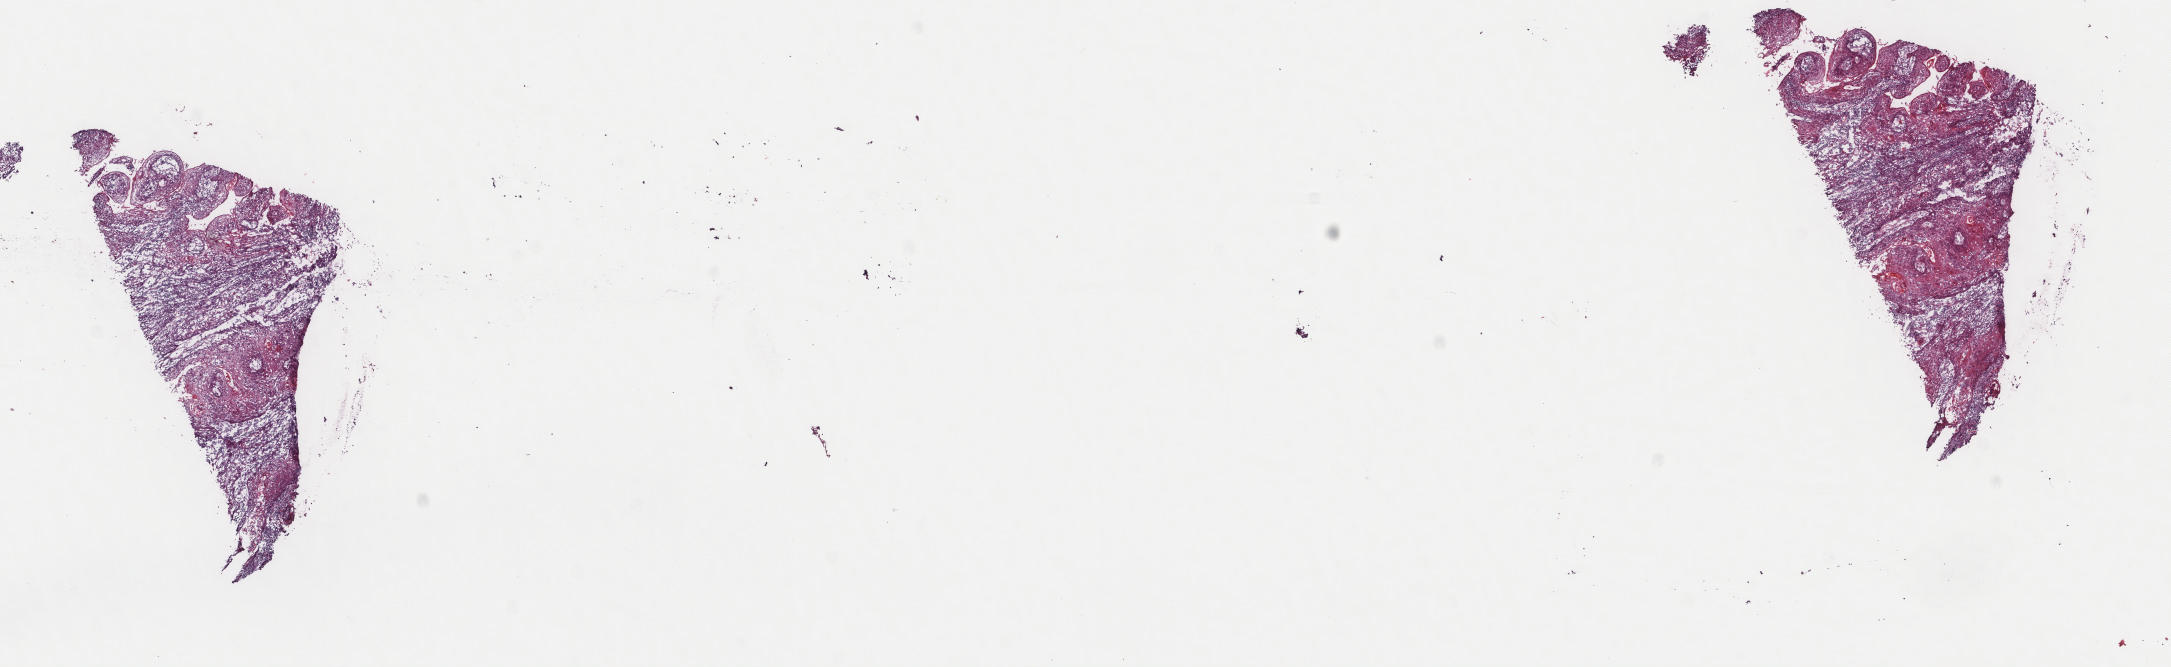
Digitized H&E-stained tissue section (whole slide), a low-resolution overview of the entire scanned area, about 17.2 x 5.3 mm (slide scanned at 40x). Frozen section. Primary tumour sample from the head and neck. Female, age 60 years at initial diagnosis. Histologic grade: G2 (moderately differentiated). Composition of this section per pathologist review: tumour cells 75%, tumour nuclei 75%, normal cells 0%, stromal cells 25%, necrosis 0%. Infiltration values recorded for this section: lymphocyte infiltration 20%, monocyte infiltration 0%, neutrophil infiltration 0%.
Pathologic diagnosis: Squamous cell carcinoma, keratinizing, NOS (mouth, NOS). AJCC pathologic stage: IVA (7th edition). Lymph nodes positive (case pathology): 0 of 64 examined. Laterality: right.